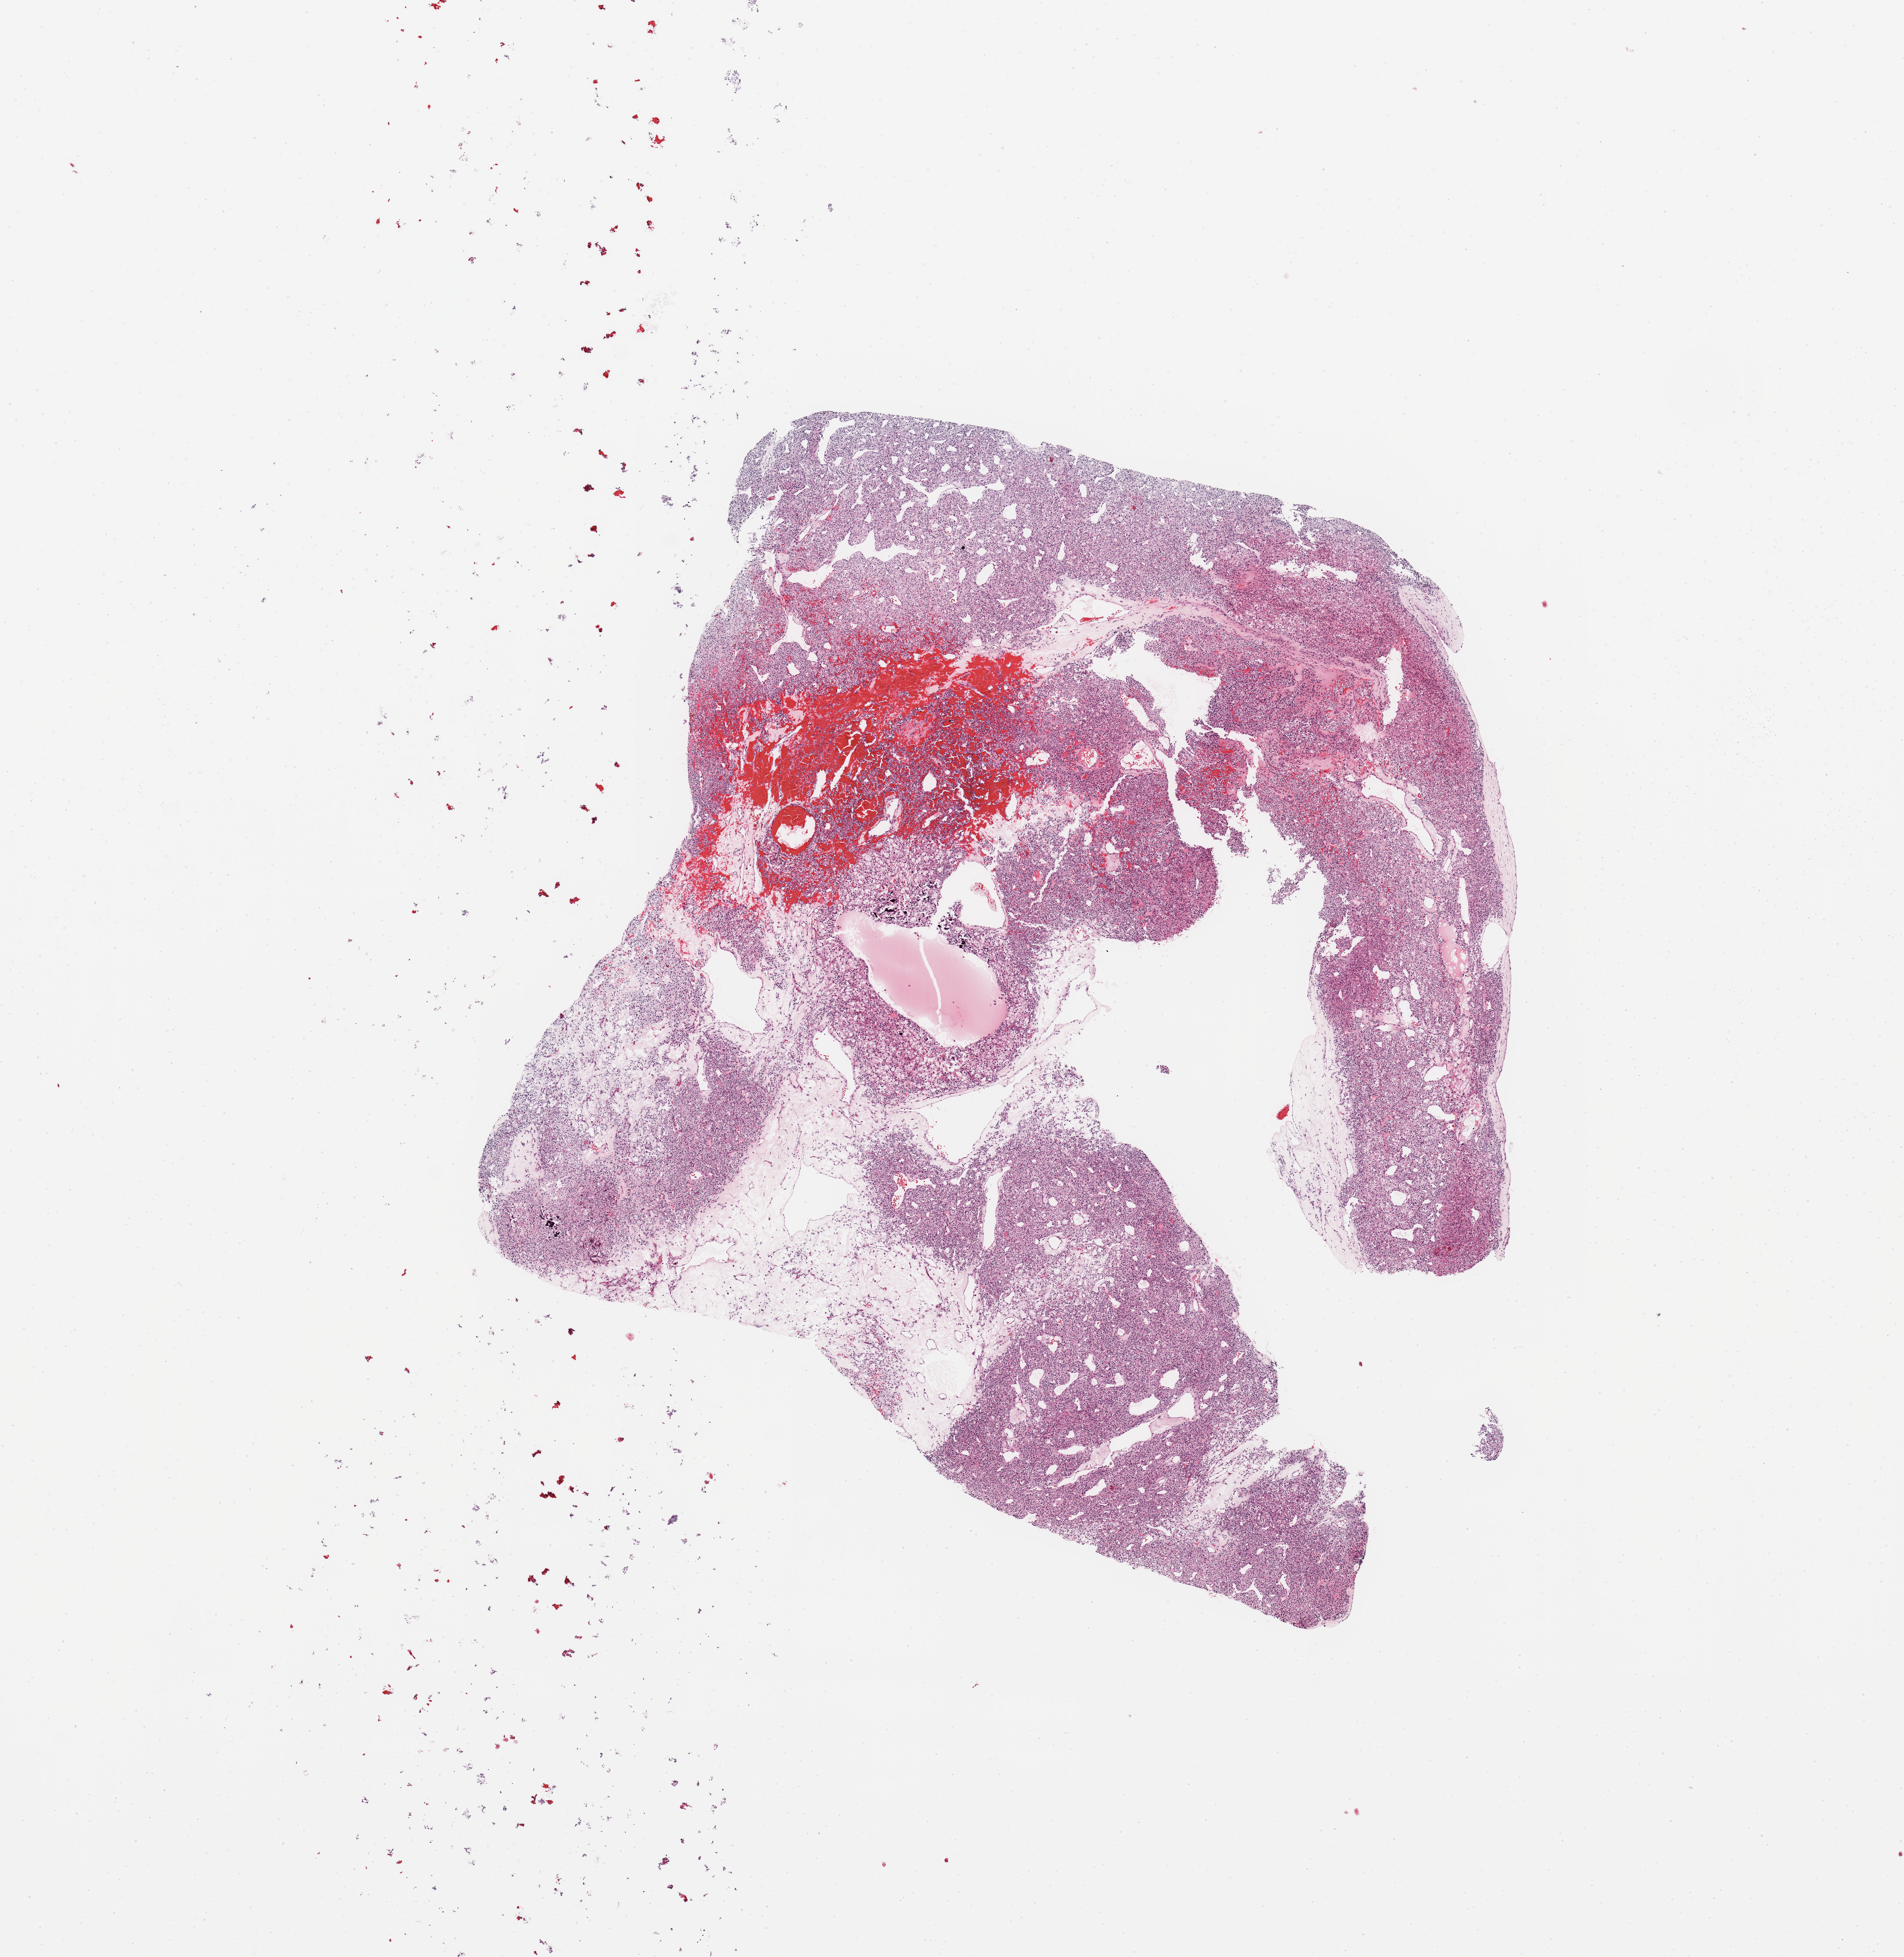
Whole-slide histology image, Hematoxylin and eosin (H&E) stained, whole scanned area (about 11.8 x 12.1 mm, from a 20x scan) shown as a low-resolution overview; tumour tissue sample, sampled site: kidney. Male, 89 y/o. Histologic grade: G2 (moderately differentiated). Composition of this section per pathologist review: tumour nuclei 80%, necrosis 10%.
Primary tumour site (as recorded): lower pole. Histologic diagnosis: Renal cell carcinoma, NOS. AJCC pathologic stage: III.